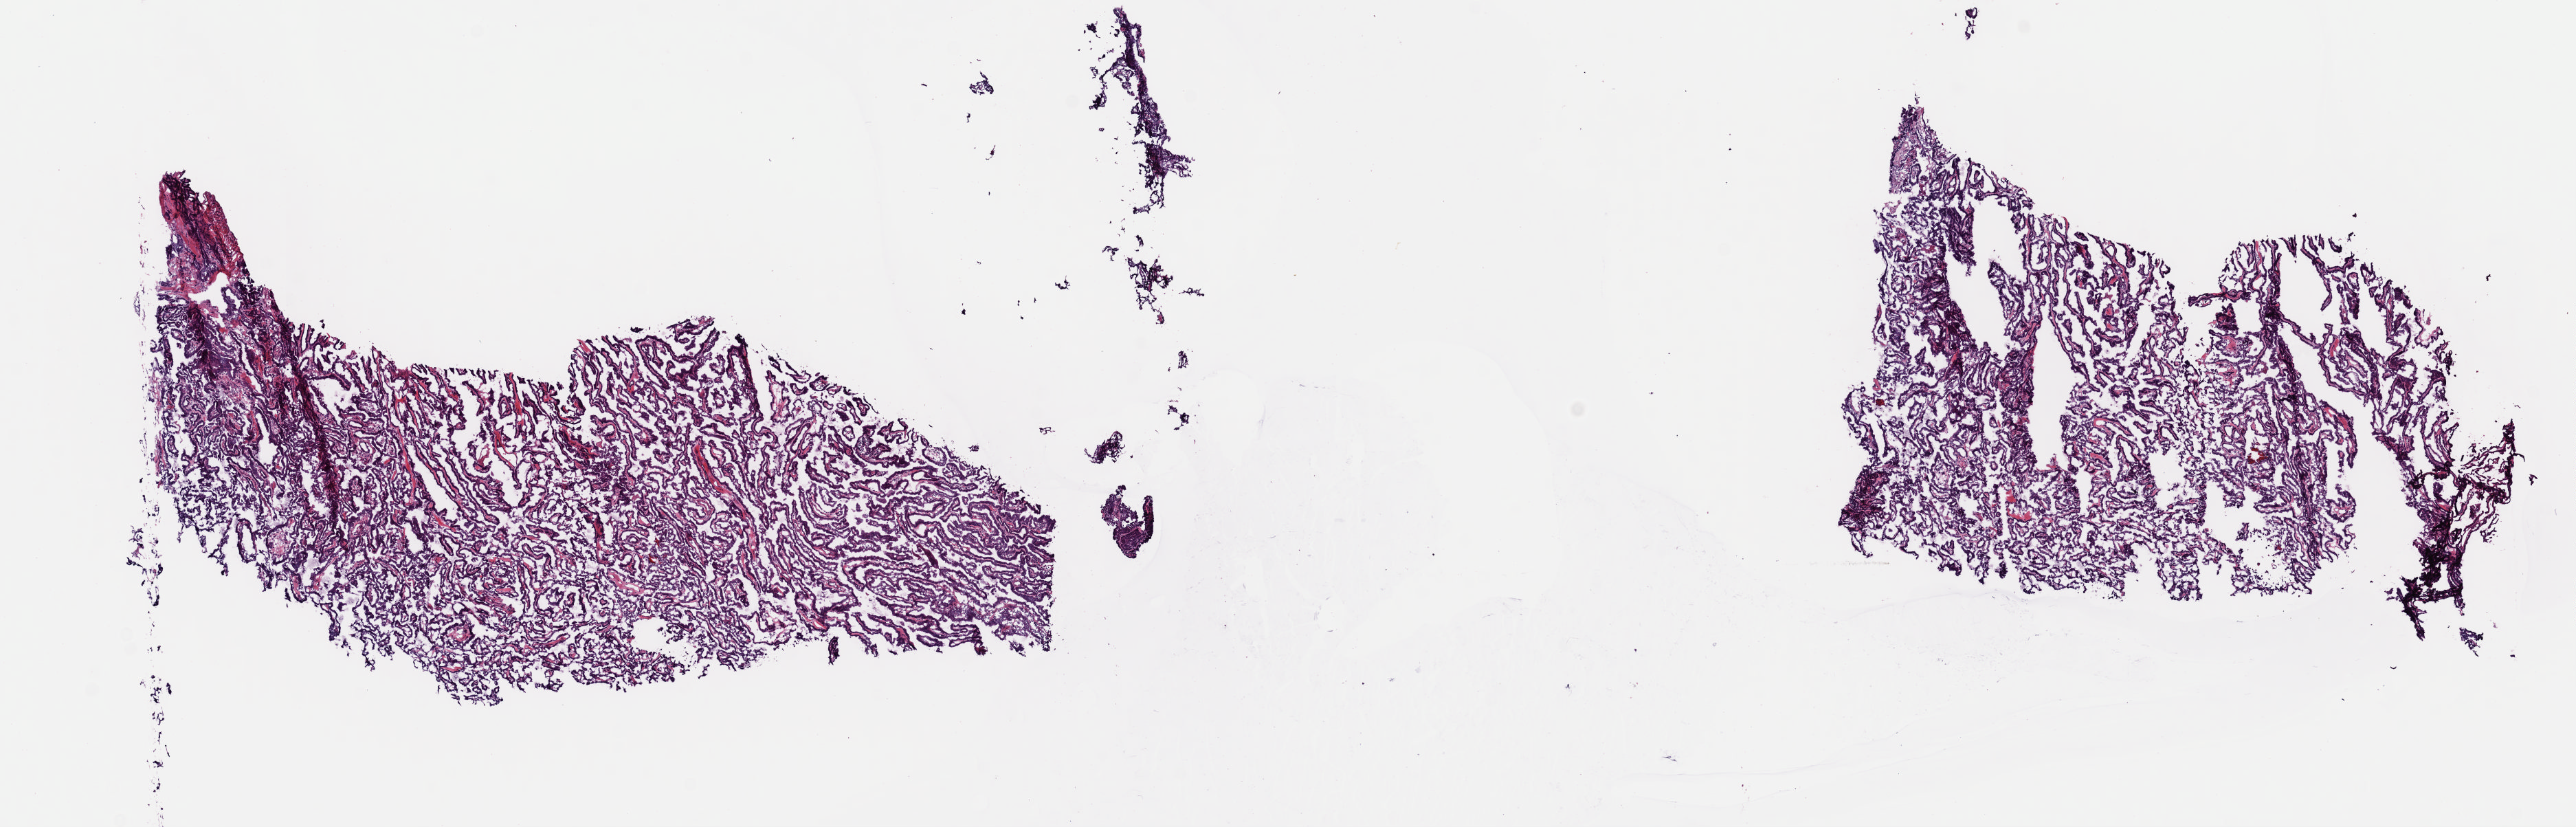
Digitized H&E-stained tissue section (whole slide), shown as a low-resolution overview of the whole scanned area (about 14.8 x 4.8 mm, from a 40x scan). Frozen section. Thyroid, primary tumour sample. Female, age 51 years at initial diagnosis. Composition of this section per pathologist review: tumour cells 100%, tumour nuclei 85%, normal cells 0%, stromal cells 0%, necrosis 0%. Inflammatory infiltration, as recorded: lymphocyte infiltration 0%, monocyte infiltration 0%, neutrophil infiltration 0%.
AJCC pathologic stage: III (7th edition). Histologic diagnosis: Papillary carcinoma, columnar cell (thyroid gland).